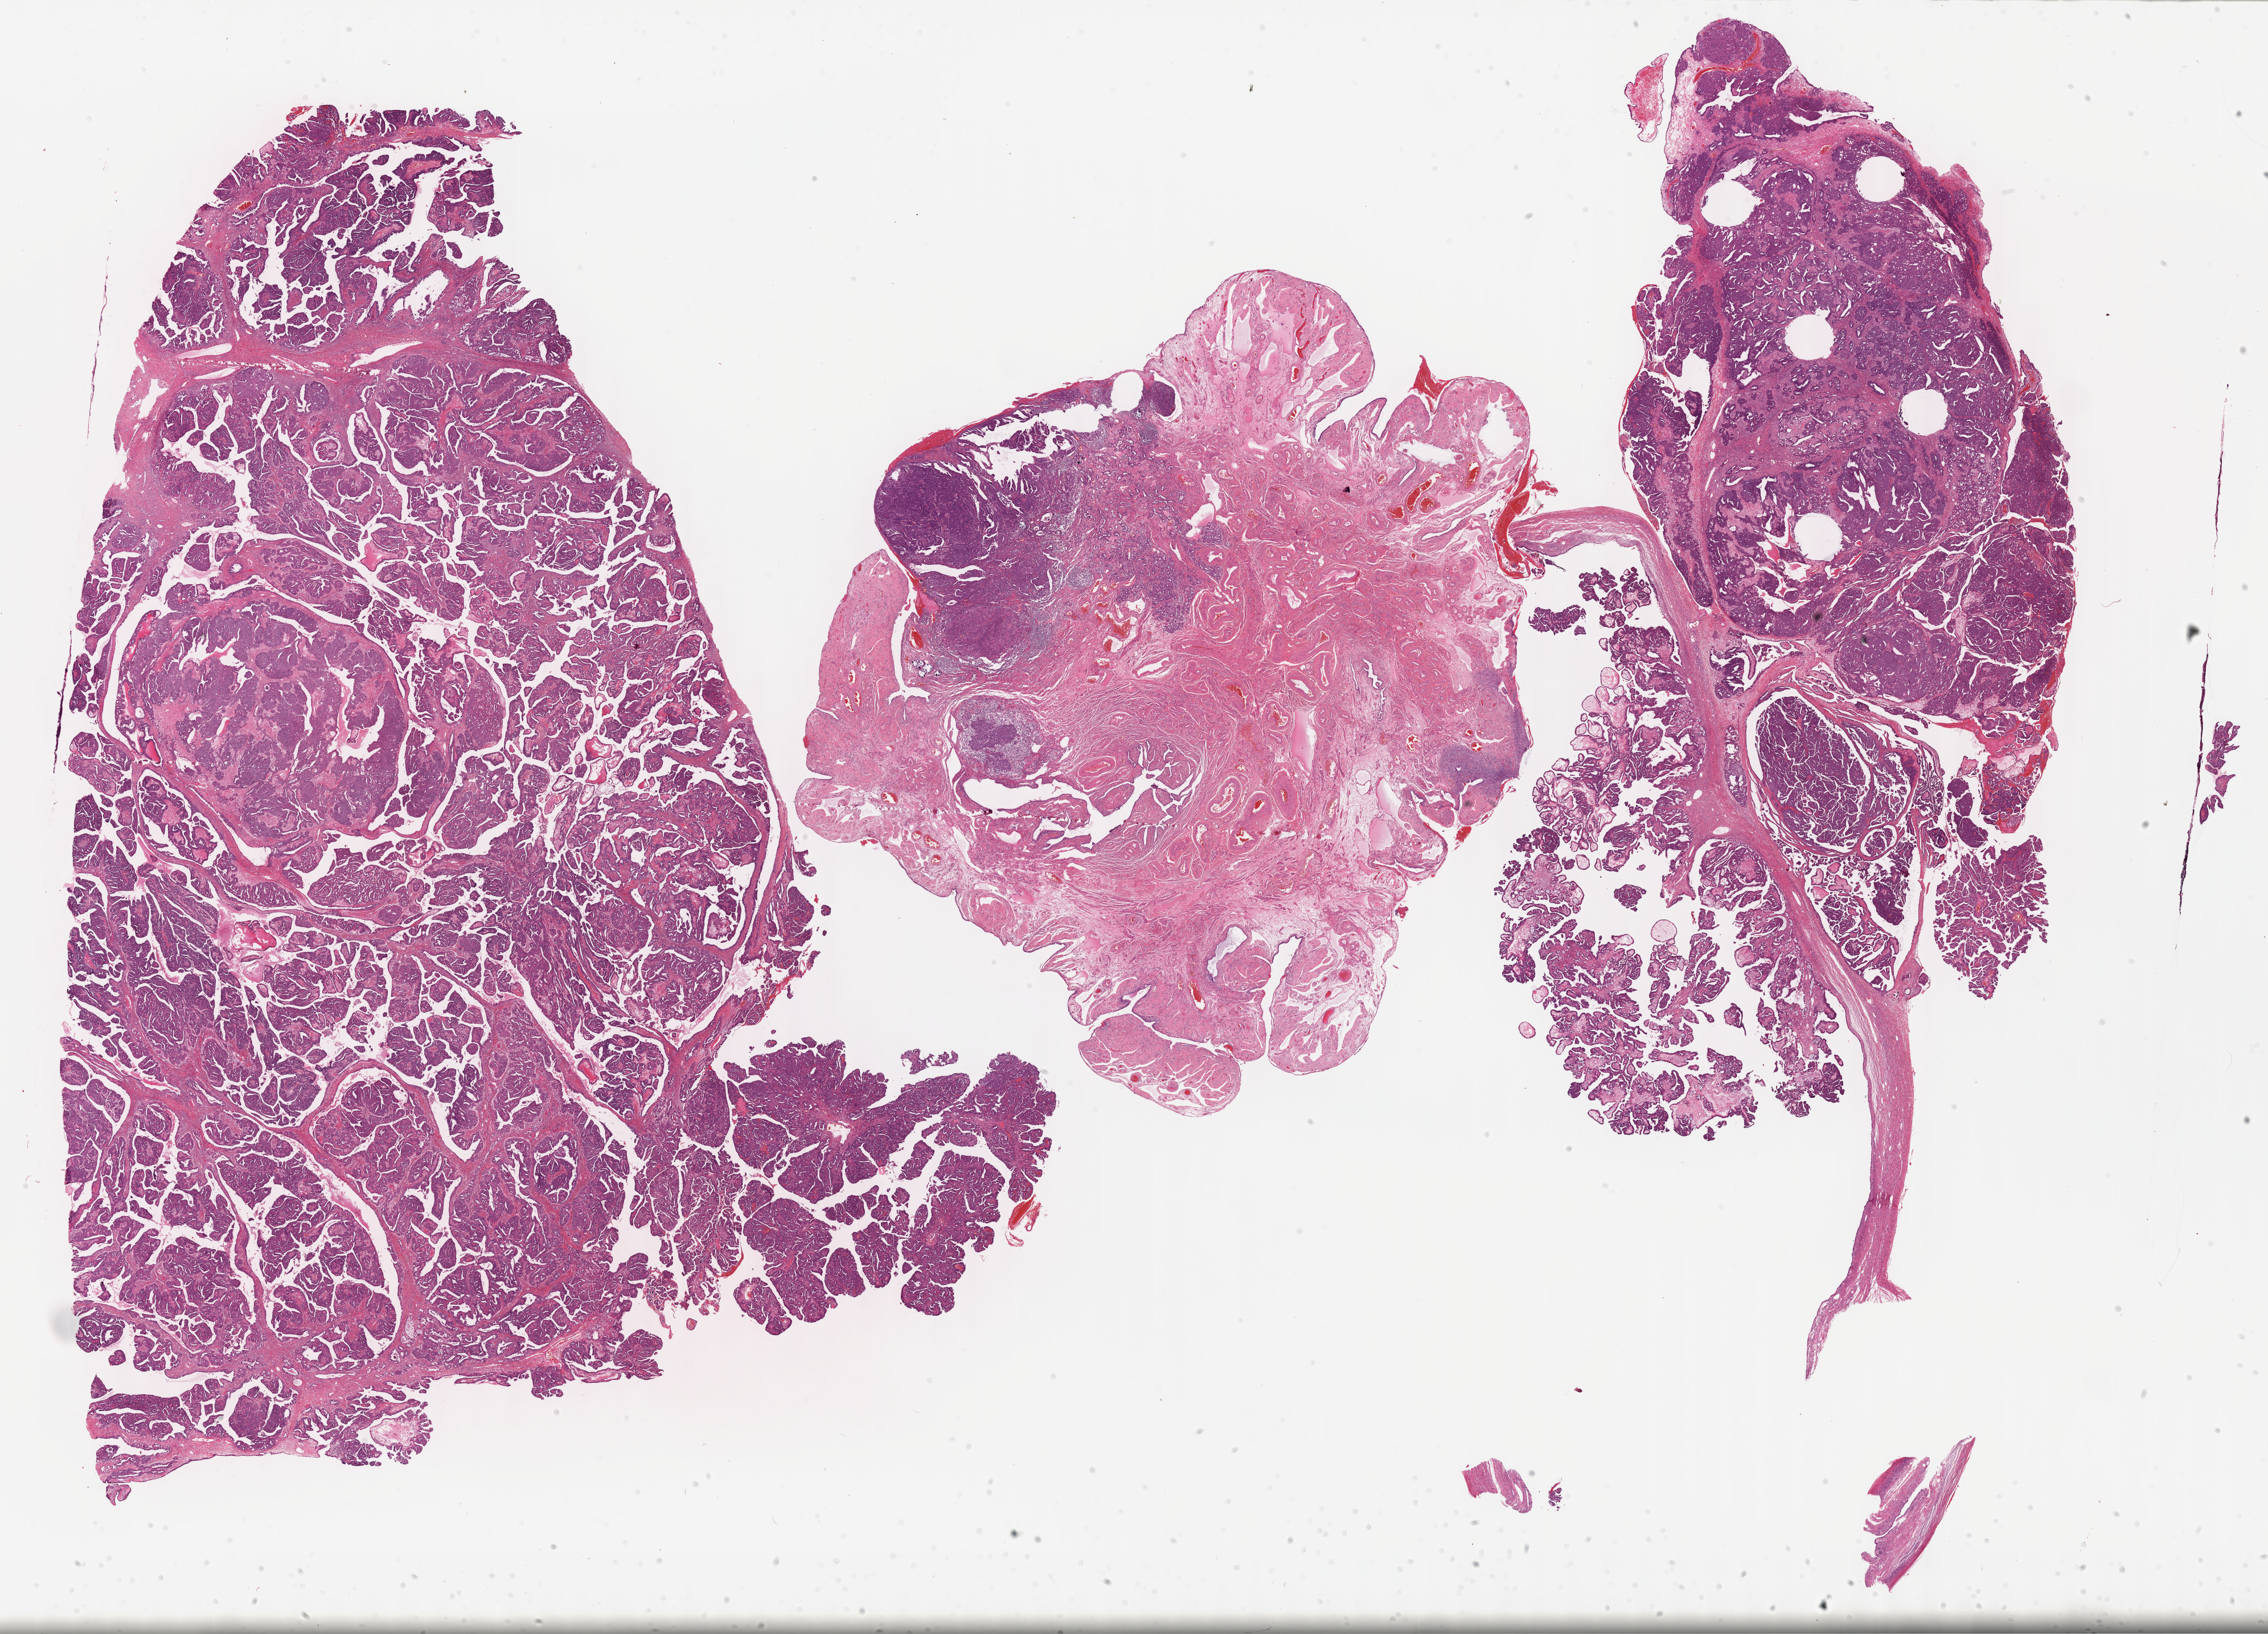
Digitized H&E tissue section (whole slide), a low-resolution overview of the entire scanned area, about 32.2 x 23.2 mm; formalin-fixed paraffin-embedded (FFPE) diagnostic section; sample: primary tumour, ovary. Patient: female, age at initial diagnosis 58 years. Histologic grade: G3 (poorly differentiated).
Pathologic diagnosis: Serous cystadenocarcinoma, NOS. FIGO stage: IV. Laterality: right.